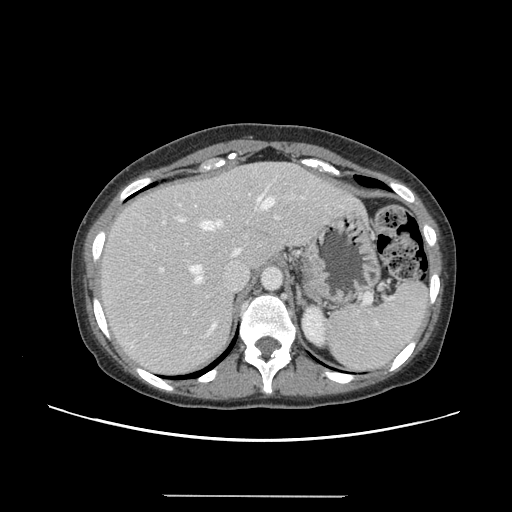
Contrast-enhanced abdominal CT, one axial slice; slice 108 of 144 in the series (ordered by position); 120 kVp; intravenous contrast given; soft-tissue window (W 400 / L 40 HU); 2.5 mm slice thickness; 512 × 512 image matrix, field of view 380 × 380 mm. Female patient, age 53 years. From the clinical record (not read from this slice): diagnosis: colorectal cancer liver metastases, imaged before liver resection; multiple liver metastases: yes; largest metastasis: 1.1 cm.
Annotated regions visible in this slice (outlined manually by an expert reader):
- hepatic veins: box from (x=179, y=195) to (x=275, y=283) px
- liver: (x=100, y=162)–(x=361, y=374)
- planned liver remnant (the part of the liver to remain after resection): (x=91, y=162)–(x=297, y=301)
- portal vein (with intrahepatic branches): (x=159, y=216)–(x=279, y=273)